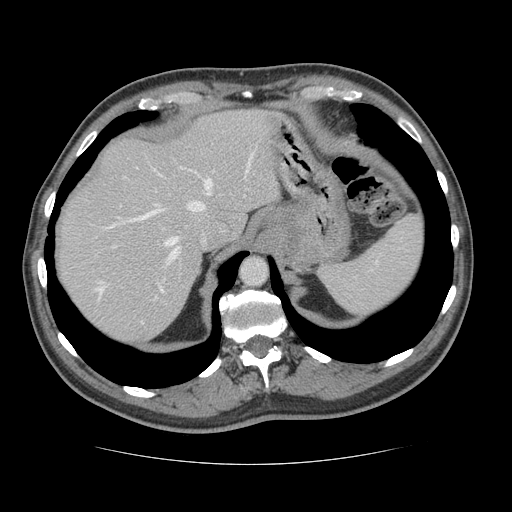
Contrast-enhanced abdominal CT, one axial slice; slice 103 of 134 in the series (ordered by position); reconstruction kernel STANDARD; intravenous contrast given; soft-tissue window (W 400 / L 40 HU); 512 × 512 image matrix, field of view 377 × 377 mm. Male patient, age 68 years. From the clinical record (not read from this slice): diagnosis: colorectal cancer liver metastases, imaged before liver resection; multiple liver metastases: yes; largest metastasis: 2.2 cm; disease in both lobes: no.
Outlined on this slice (expert manual segmentation):
- hepatic veins: bounding box [x1, y1, x2, y2] px = [96, 152, 254, 297]
- liver: [56, 109, 278, 345]
- planned liver remnant (the part of the liver to remain after resection): [56, 109, 278, 321]
- portal vein (with intrahepatic branches): [113, 246, 157, 298]